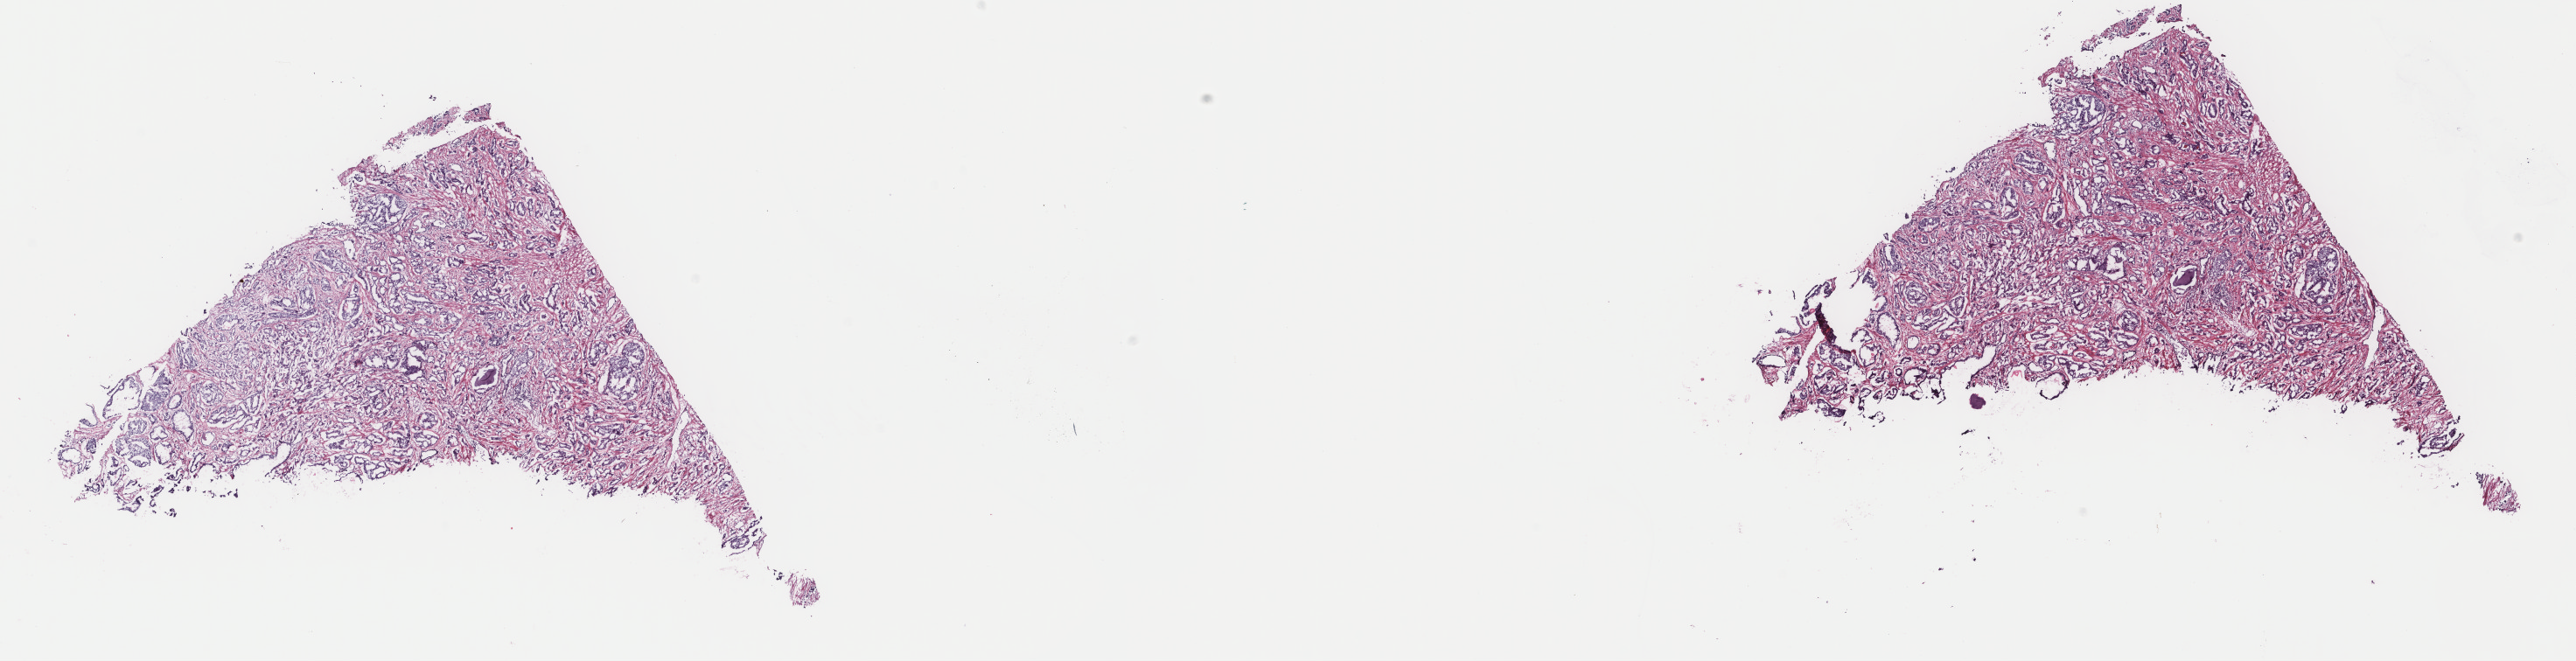
Whole-slide histology image, Hematoxylin and eosin (H&E) stained, shown as a low-resolution overview of the whole scanned area (about 23.4 x 6.0 mm, from a 40x scan). Frozen section from the top of the tissue portion. Sample: primary tumour, prostate. Male patient; age at initial diagnosis 67 years. Gleason score: 9 (4+5). Pathologist review of this section (percent, as recorded): tumour cells 80%, tumour nuclei 80%, normal cells 0%, stromal cells 20%, necrosis 0%. Inflammatory infiltration, as recorded: lymphocyte infiltration 40%, monocyte infiltration 20%, neutrophil infiltration 20%.
- lymph nodes positive (case pathology): 0 of 17 examined
- histologic diagnosis: Adenocarcinoma, NOS (prostate gland)